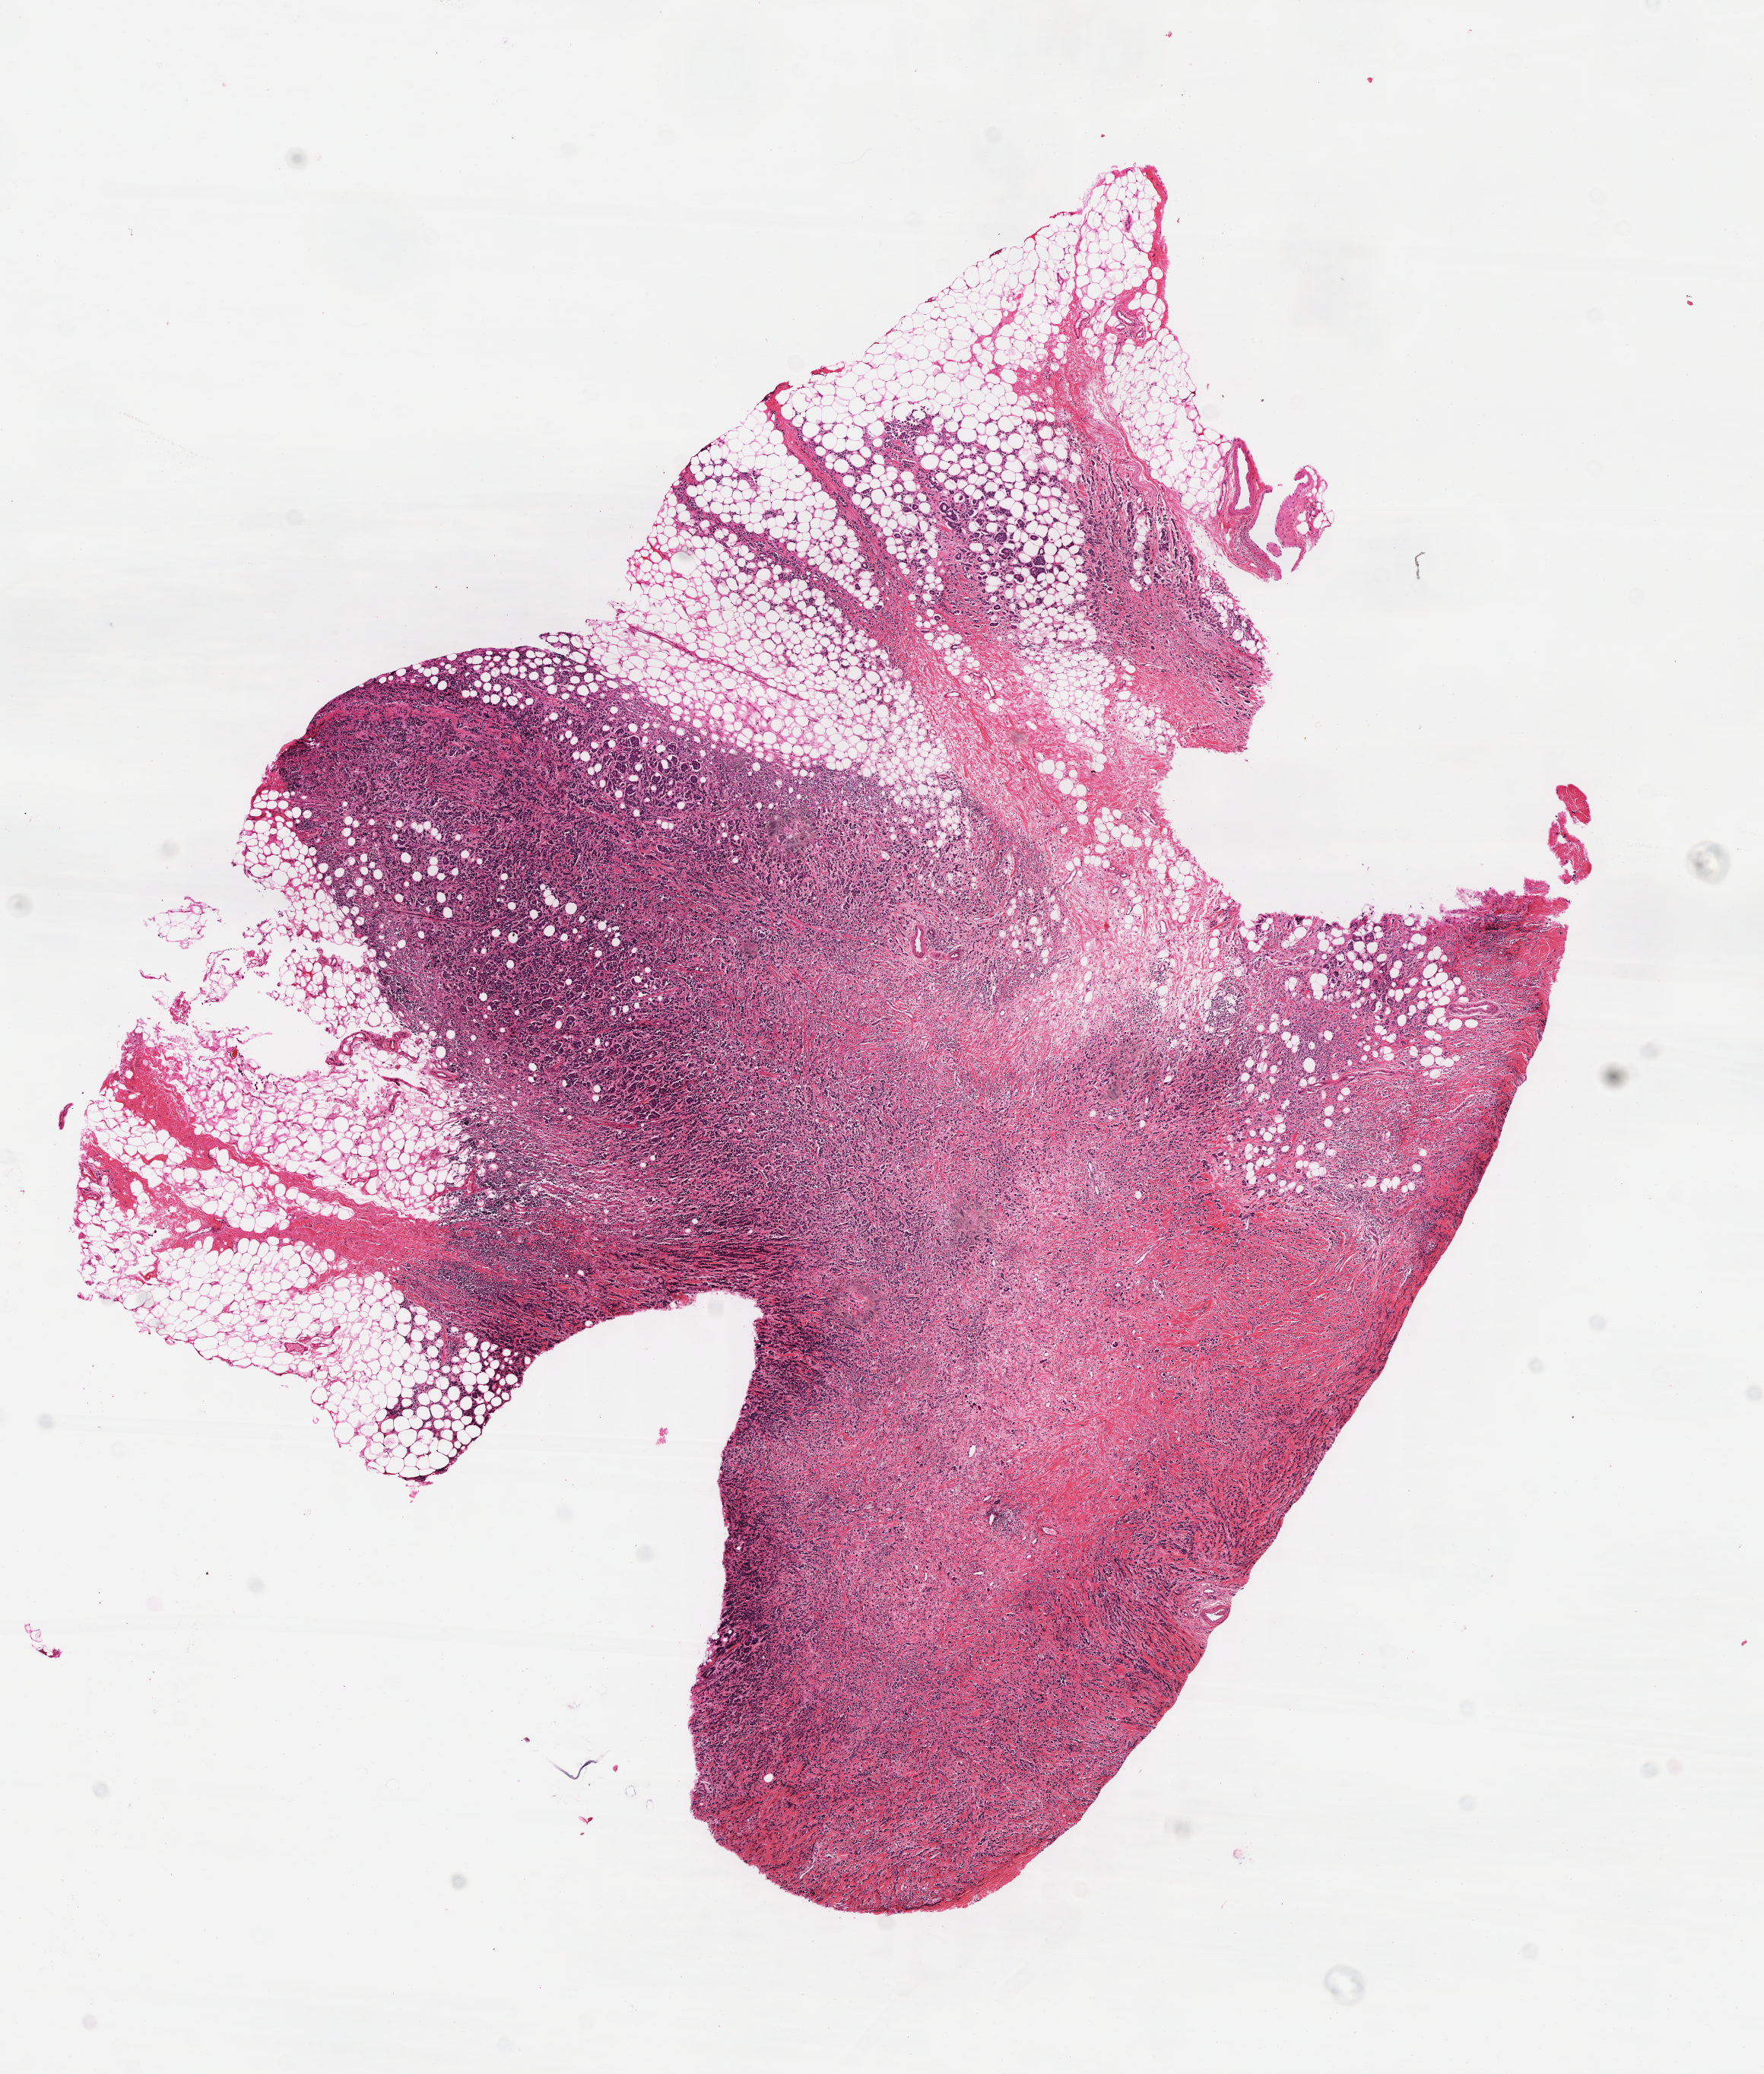
Digitized H&E tissue section (whole slide), shown as a low-resolution overview of the whole scanned area (about 9.1 x 10.7 mm, acquisition: 40x scan), formalin-fixed paraffin-embedded (FFPE) diagnostic section, sample: primary tumour, breast. Patient: female, age at initial diagnosis 41 years.
AJCC pathologic stage: IIA. TNM: T2 N0 M0. Laterality: left. Pathologic diagnosis: Lobular carcinoma, NOS. Lymph nodes positive (case pathology): 0 of 1 examined.